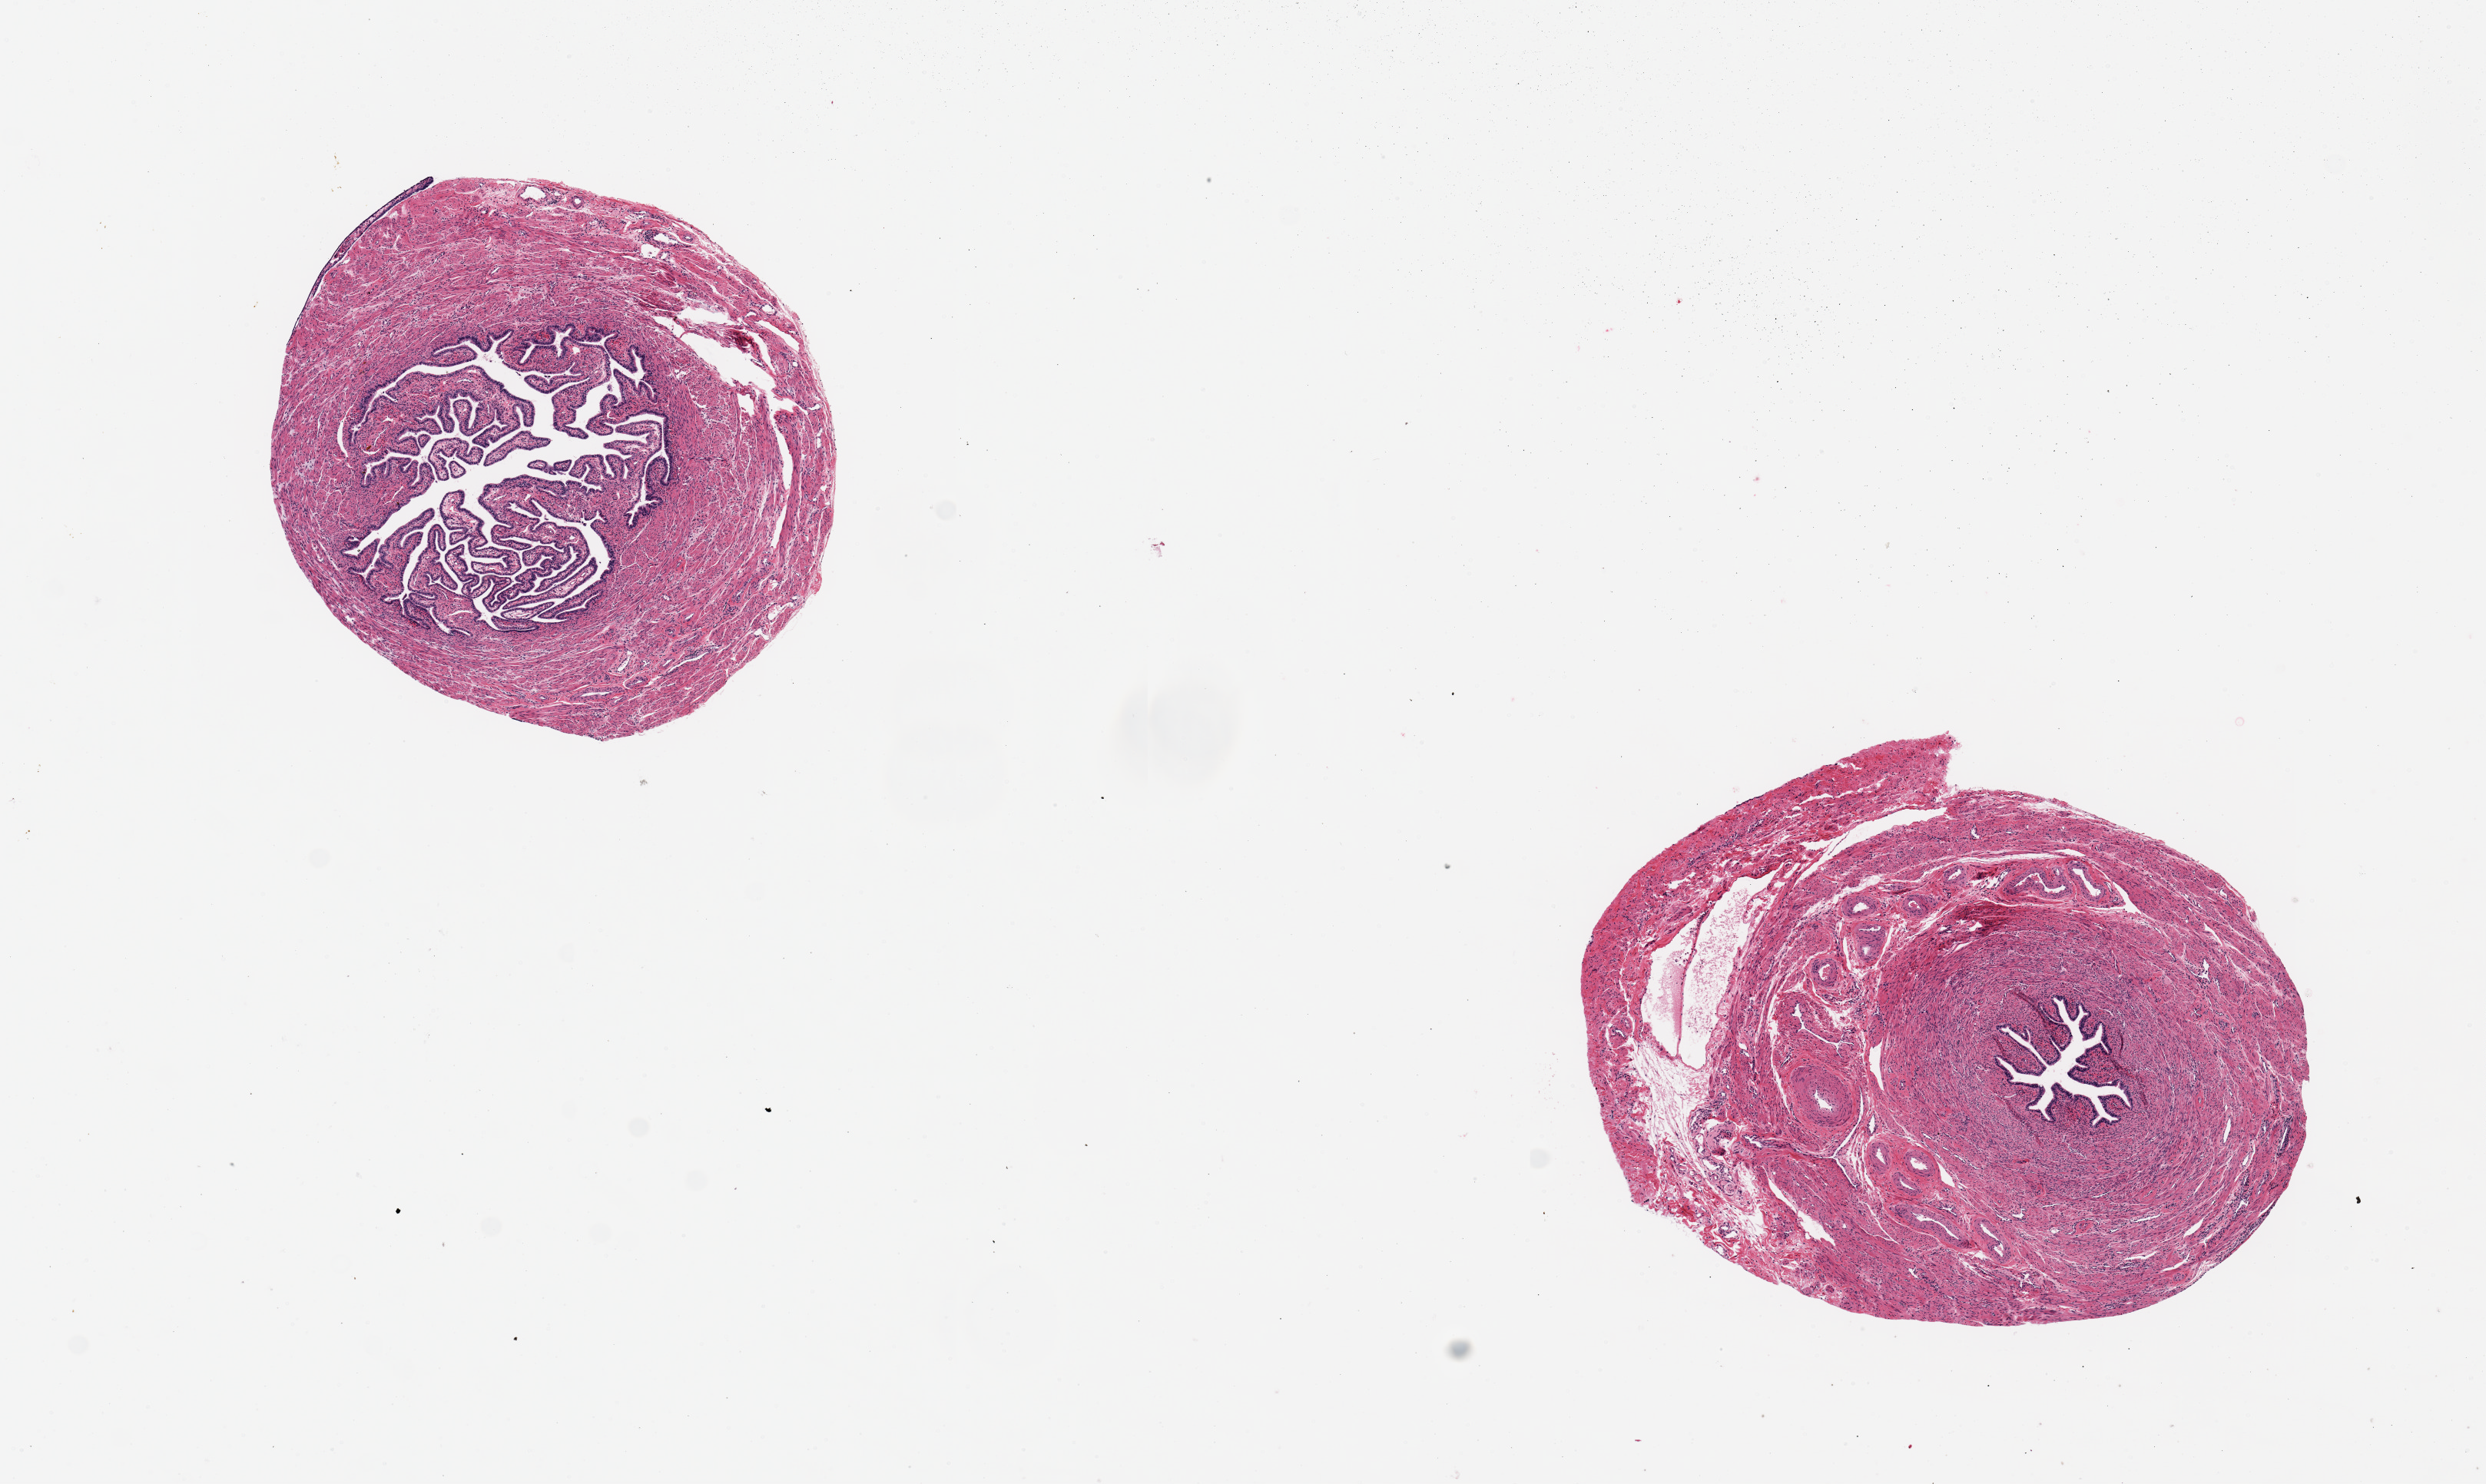
Digitized H&E-stained section — a low-resolution overview of the entire scanned area, about 12.8 x 7.6 mm, PAXgene-fixed, paraffin-embedded tissue, section of fallopian tube (target tissue), tissue donor sample. Donor: female.
Review note (as recorded): 2 ~ 3mm d aliquots; good clean specimens.